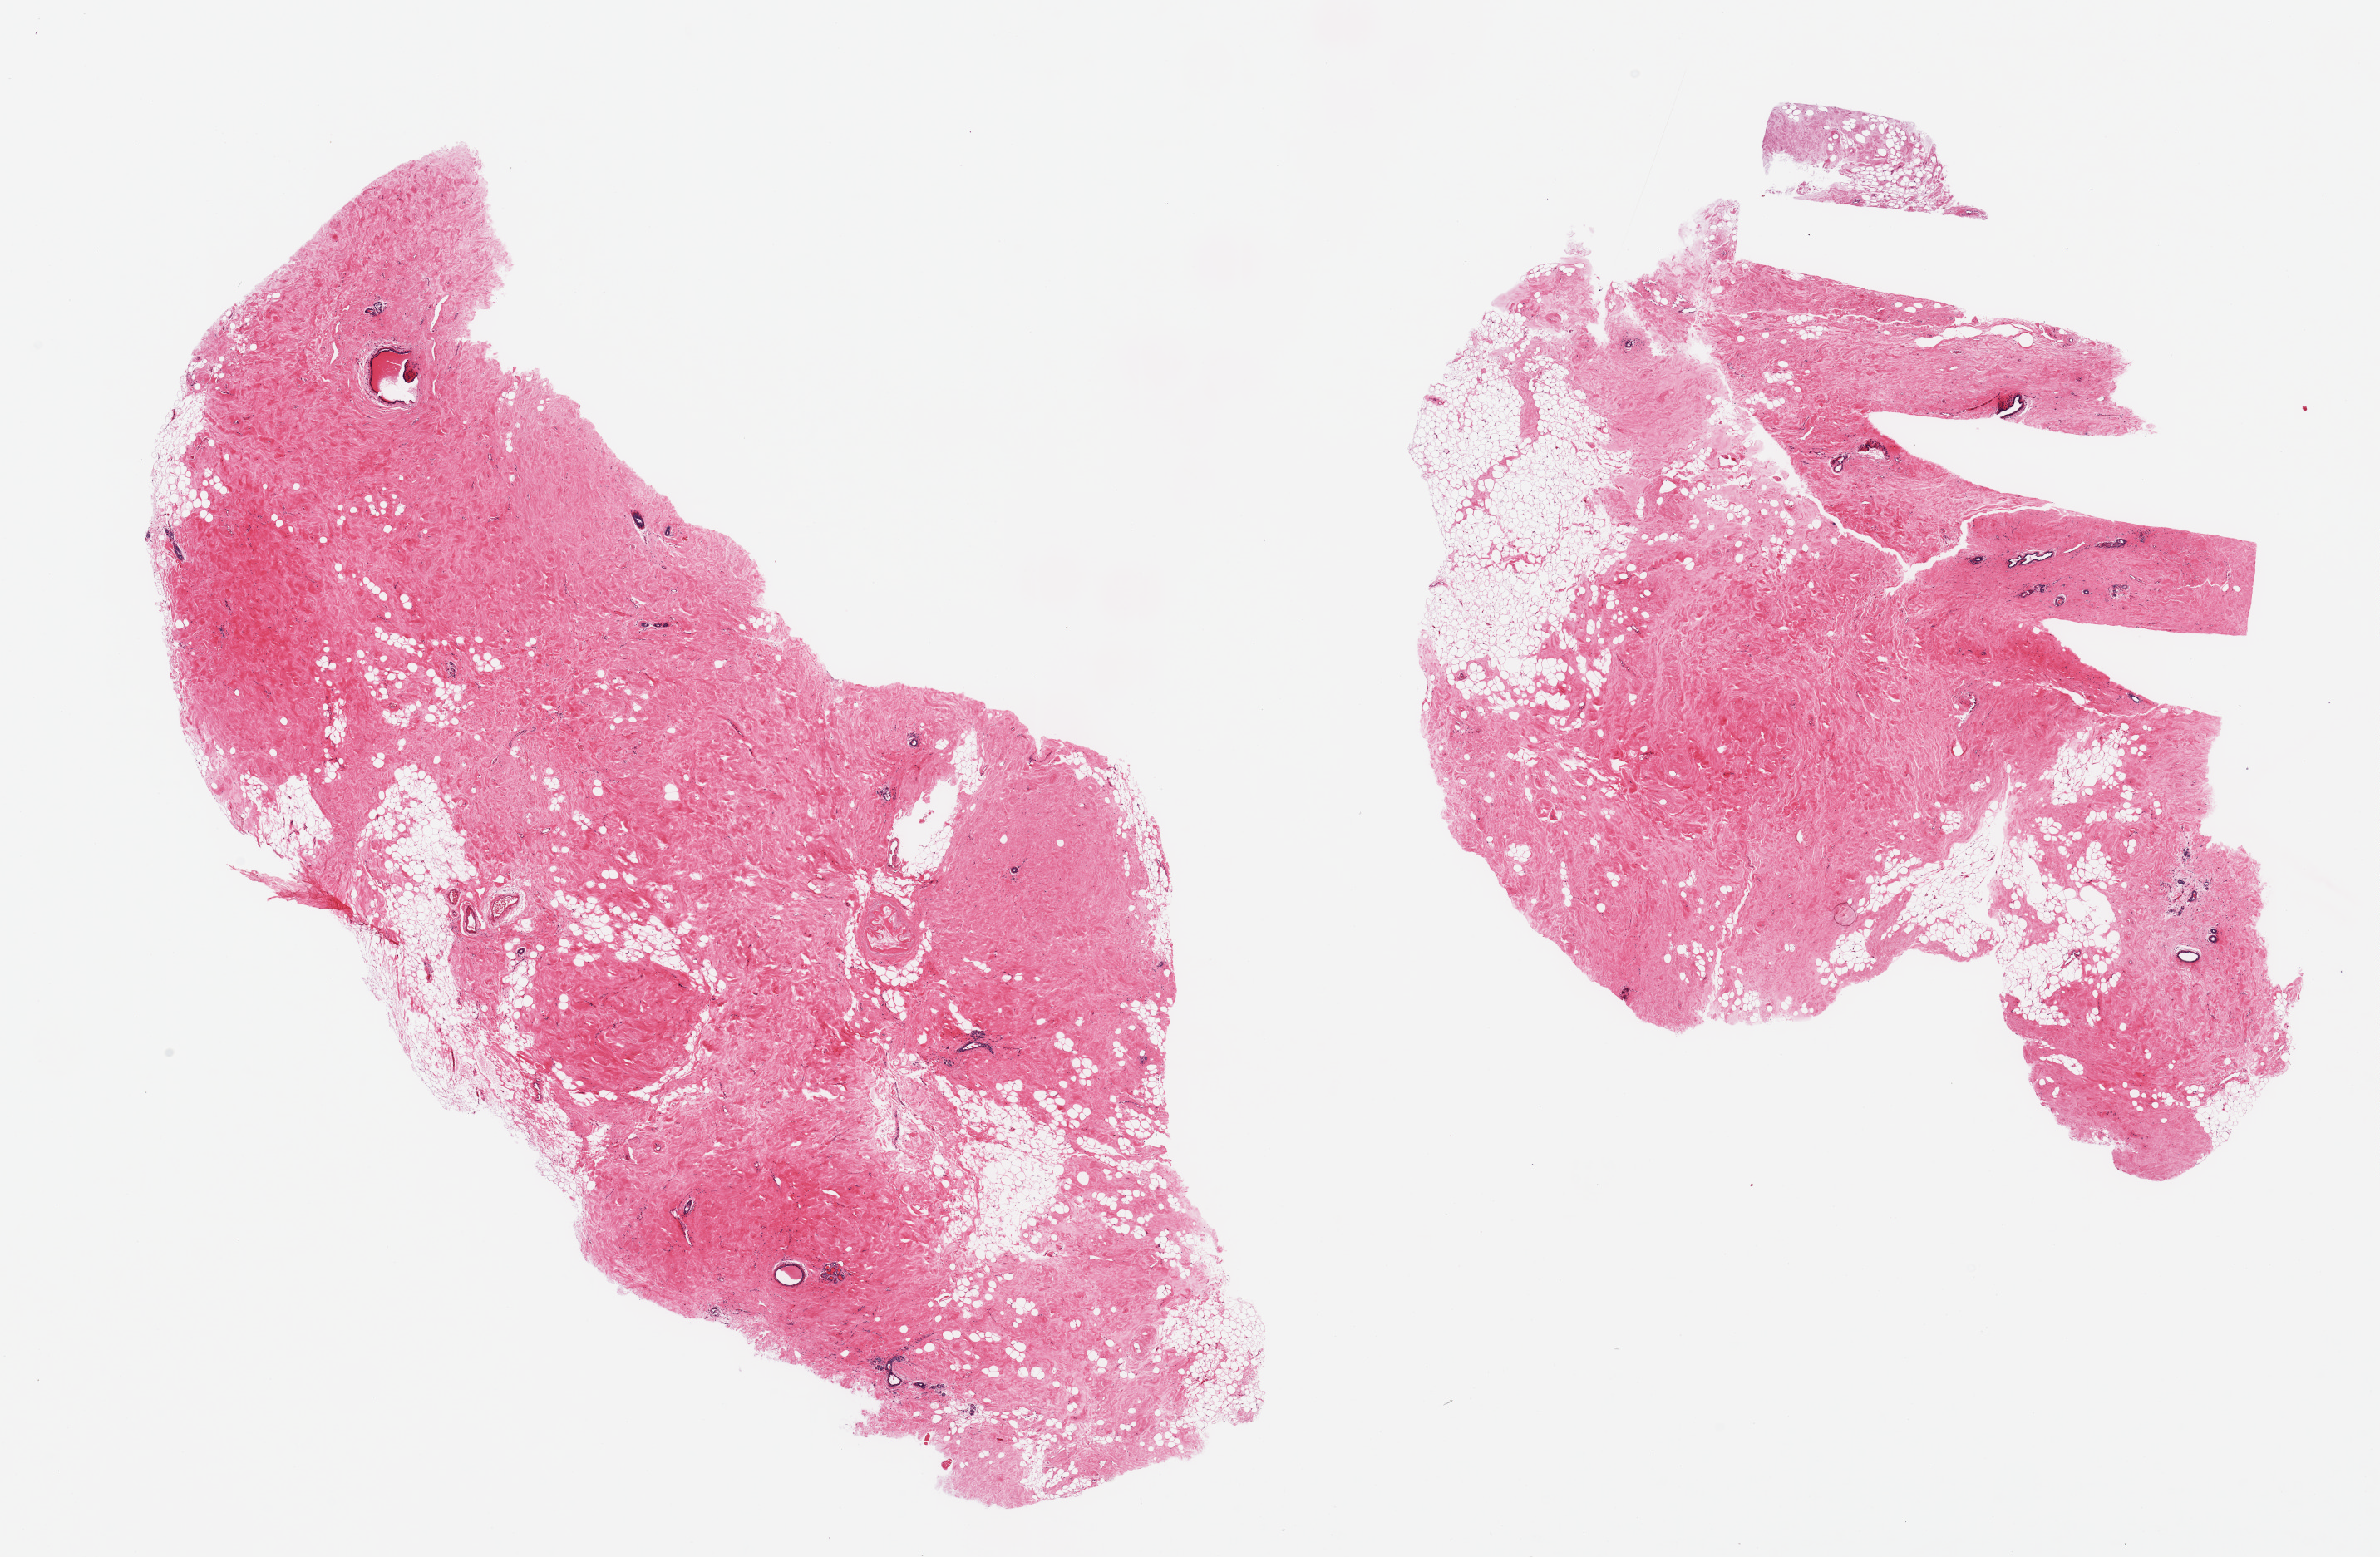
Digitized H&E-stained section, brightfield — shown as a low-resolution overview of the whole scanned area (about 22.6 x 14.8 mm, from a 20x scan), PAXgene-fixed paraffin-embedded (PFPE) section, target tissue: breast, tissue donor sample. Donor sex: female.
Pathologist's review note for this sample: 2 pieces; atrophic ducts, abundant fibrous tissue.